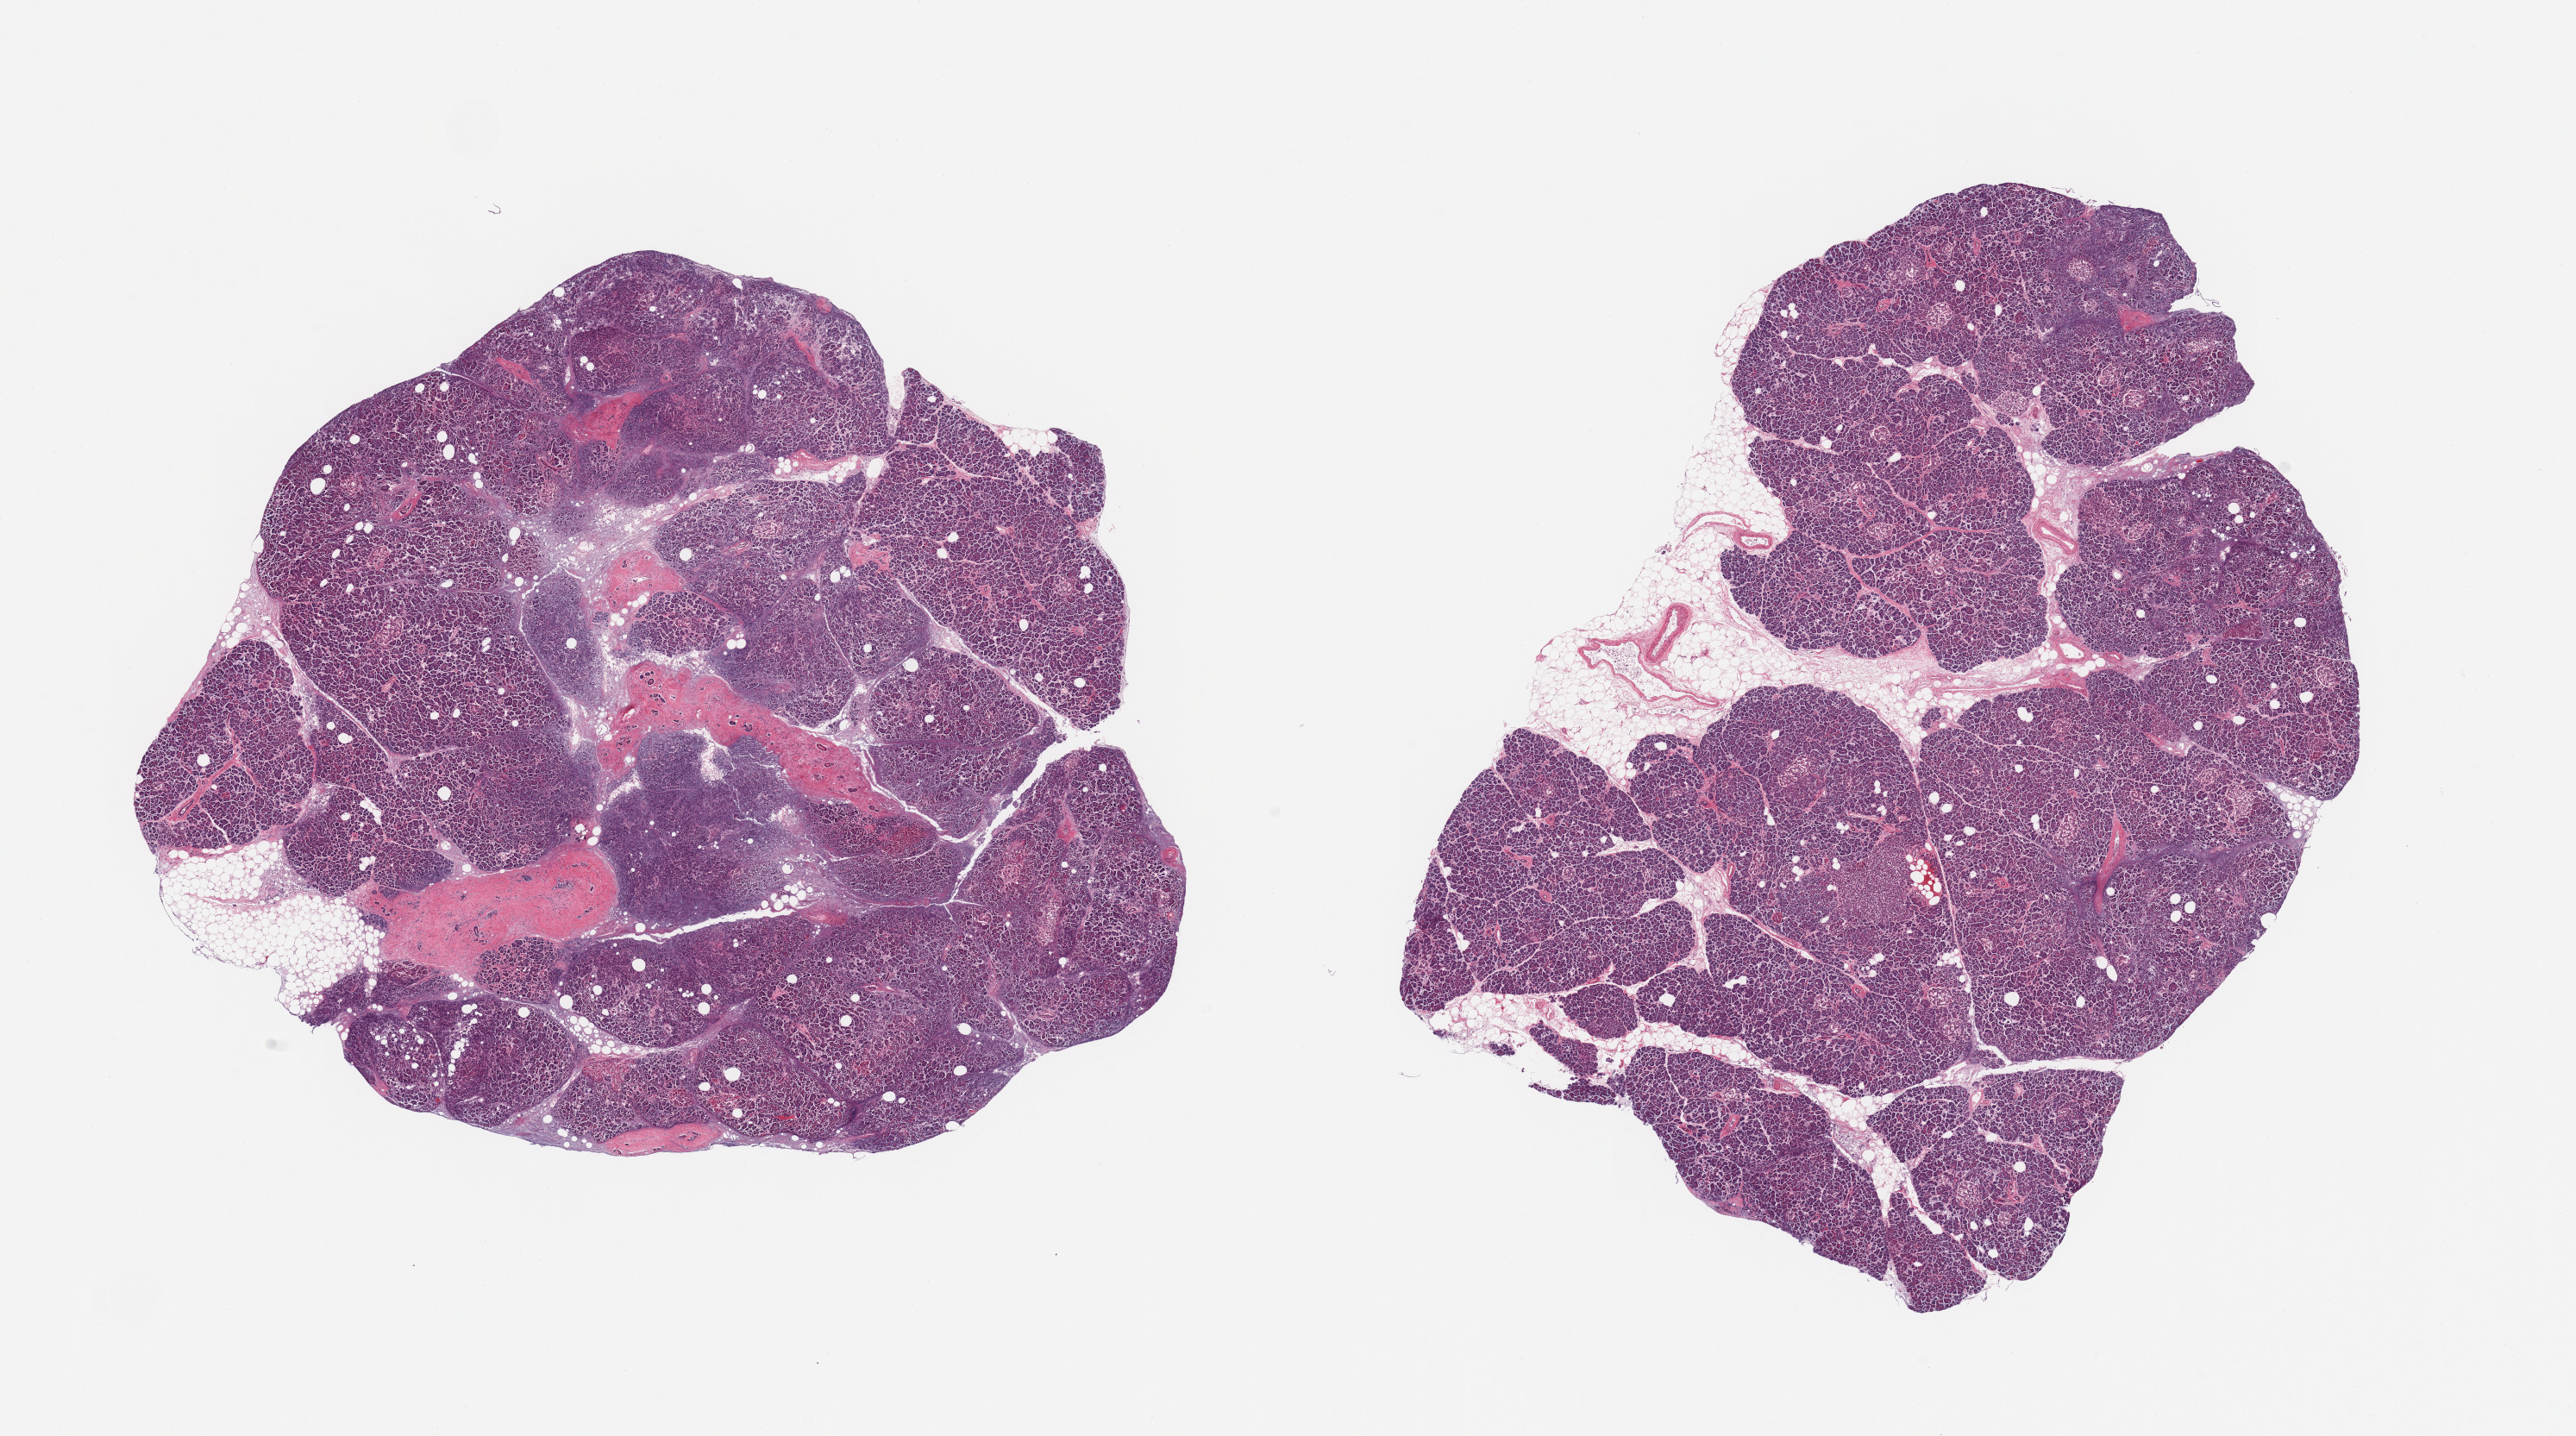
Hematoxylin and eosin (H&E) whole-slide image — a low-resolution overview of the entire scanned area, about 23.6 x 13.2 mm, PAXgene-fixed paraffin-embedded (PFPE) section, target tissue: pancreas, donor tissue sample. Donor: male.
Pathologist's review note for this sample: 2 pieces; 10 & 5% internal fat.